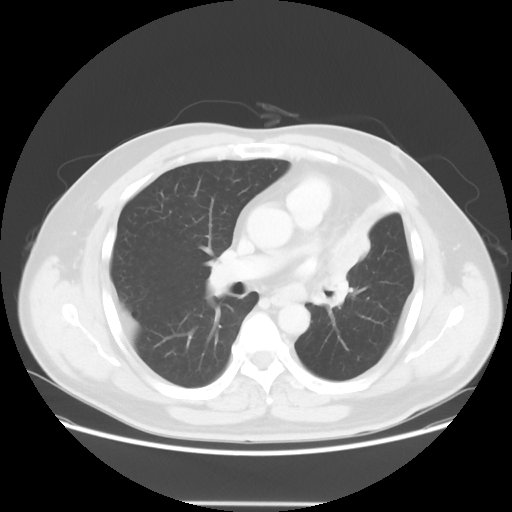
Chest CT, one axial slice. Slice 35 of 62 in the series (ordered by position). Reconstruction kernel STANDARD. Lung window (W 1500 / L -600 HU). 5 mm slice thickness. 512 × 512 image matrix, field of view 403 × 403 mm. Male patient, age 49 years. From the clinical record (not read from this slice): clinical TNM (as recorded): T3 N3 M1c.
Structures marked on this image (rectangle marked by the reading radiologist):
- lung tumour (recorded histology: squamous cell carcinoma): bounding box <297,214,373,318> (left, top, right, bottom; pixels)